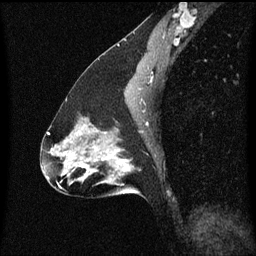
Breast MRI (dynamic contrast-enhanced), one sagittal slice; position 35 of 60 along the scan axis; dynamic contrast-enhanced series, image 2 of 3 at this slice position (ordered by acquisition); 1.5 T; TE 4.2 ms, TR 8.4 ms; 2 mm slice thickness; 256 × 256 image matrix. Patient: female, 47 years.
Outlined on this slice (semi-automatically segmented with operator editing):
- analysis volume of interest (the breast-tissue region the enhancement analysis was run in; not a lesion): bounding box <85,136,142,195> (left, top, right, bottom; pixels)
- tumour enhancement mask (voxels above the 70 % enhancement threshold inside the analysis volume of interest): <85,150,131,175>